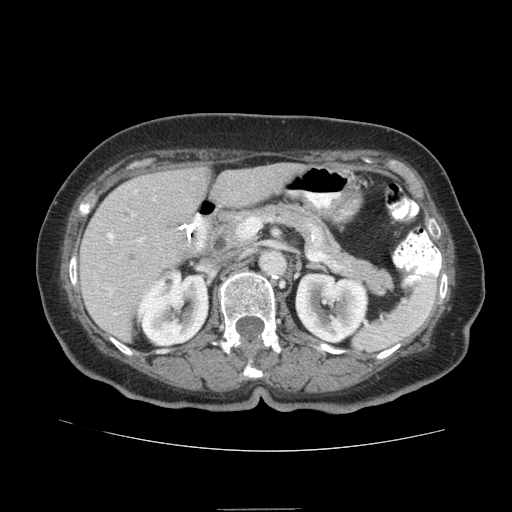
Contrast-enhanced abdominal CT (liver protocol), one axial slice. Slice 39 of 95 in the series (ordered by position). 140 kVp. Soft-tissue window (W 400 / L 40 HU). 2.5 mm slice thickness. 512 × 512 image matrix, field of view 360 × 360 mm. From the clinical record (not read from this slice): diagnosis: hepatocellular carcinoma (patient treated with transarterial chemoembolisation; whether this scan precedes or follows treatment is not stated here); TNM stage (as recorded): Stage-IVA; Child-Pugh class: B.
Outlined on this slice (semi-automatic segmentation, software-assisted and operator-edited):
- liver parenchyma outside the tumour (the mass and vessels are separate outlines, so this box may not span the whole liver): box from (x=80, y=162) to (x=302, y=340) px
- liver vessels: (x=107, y=224)–(x=205, y=315)